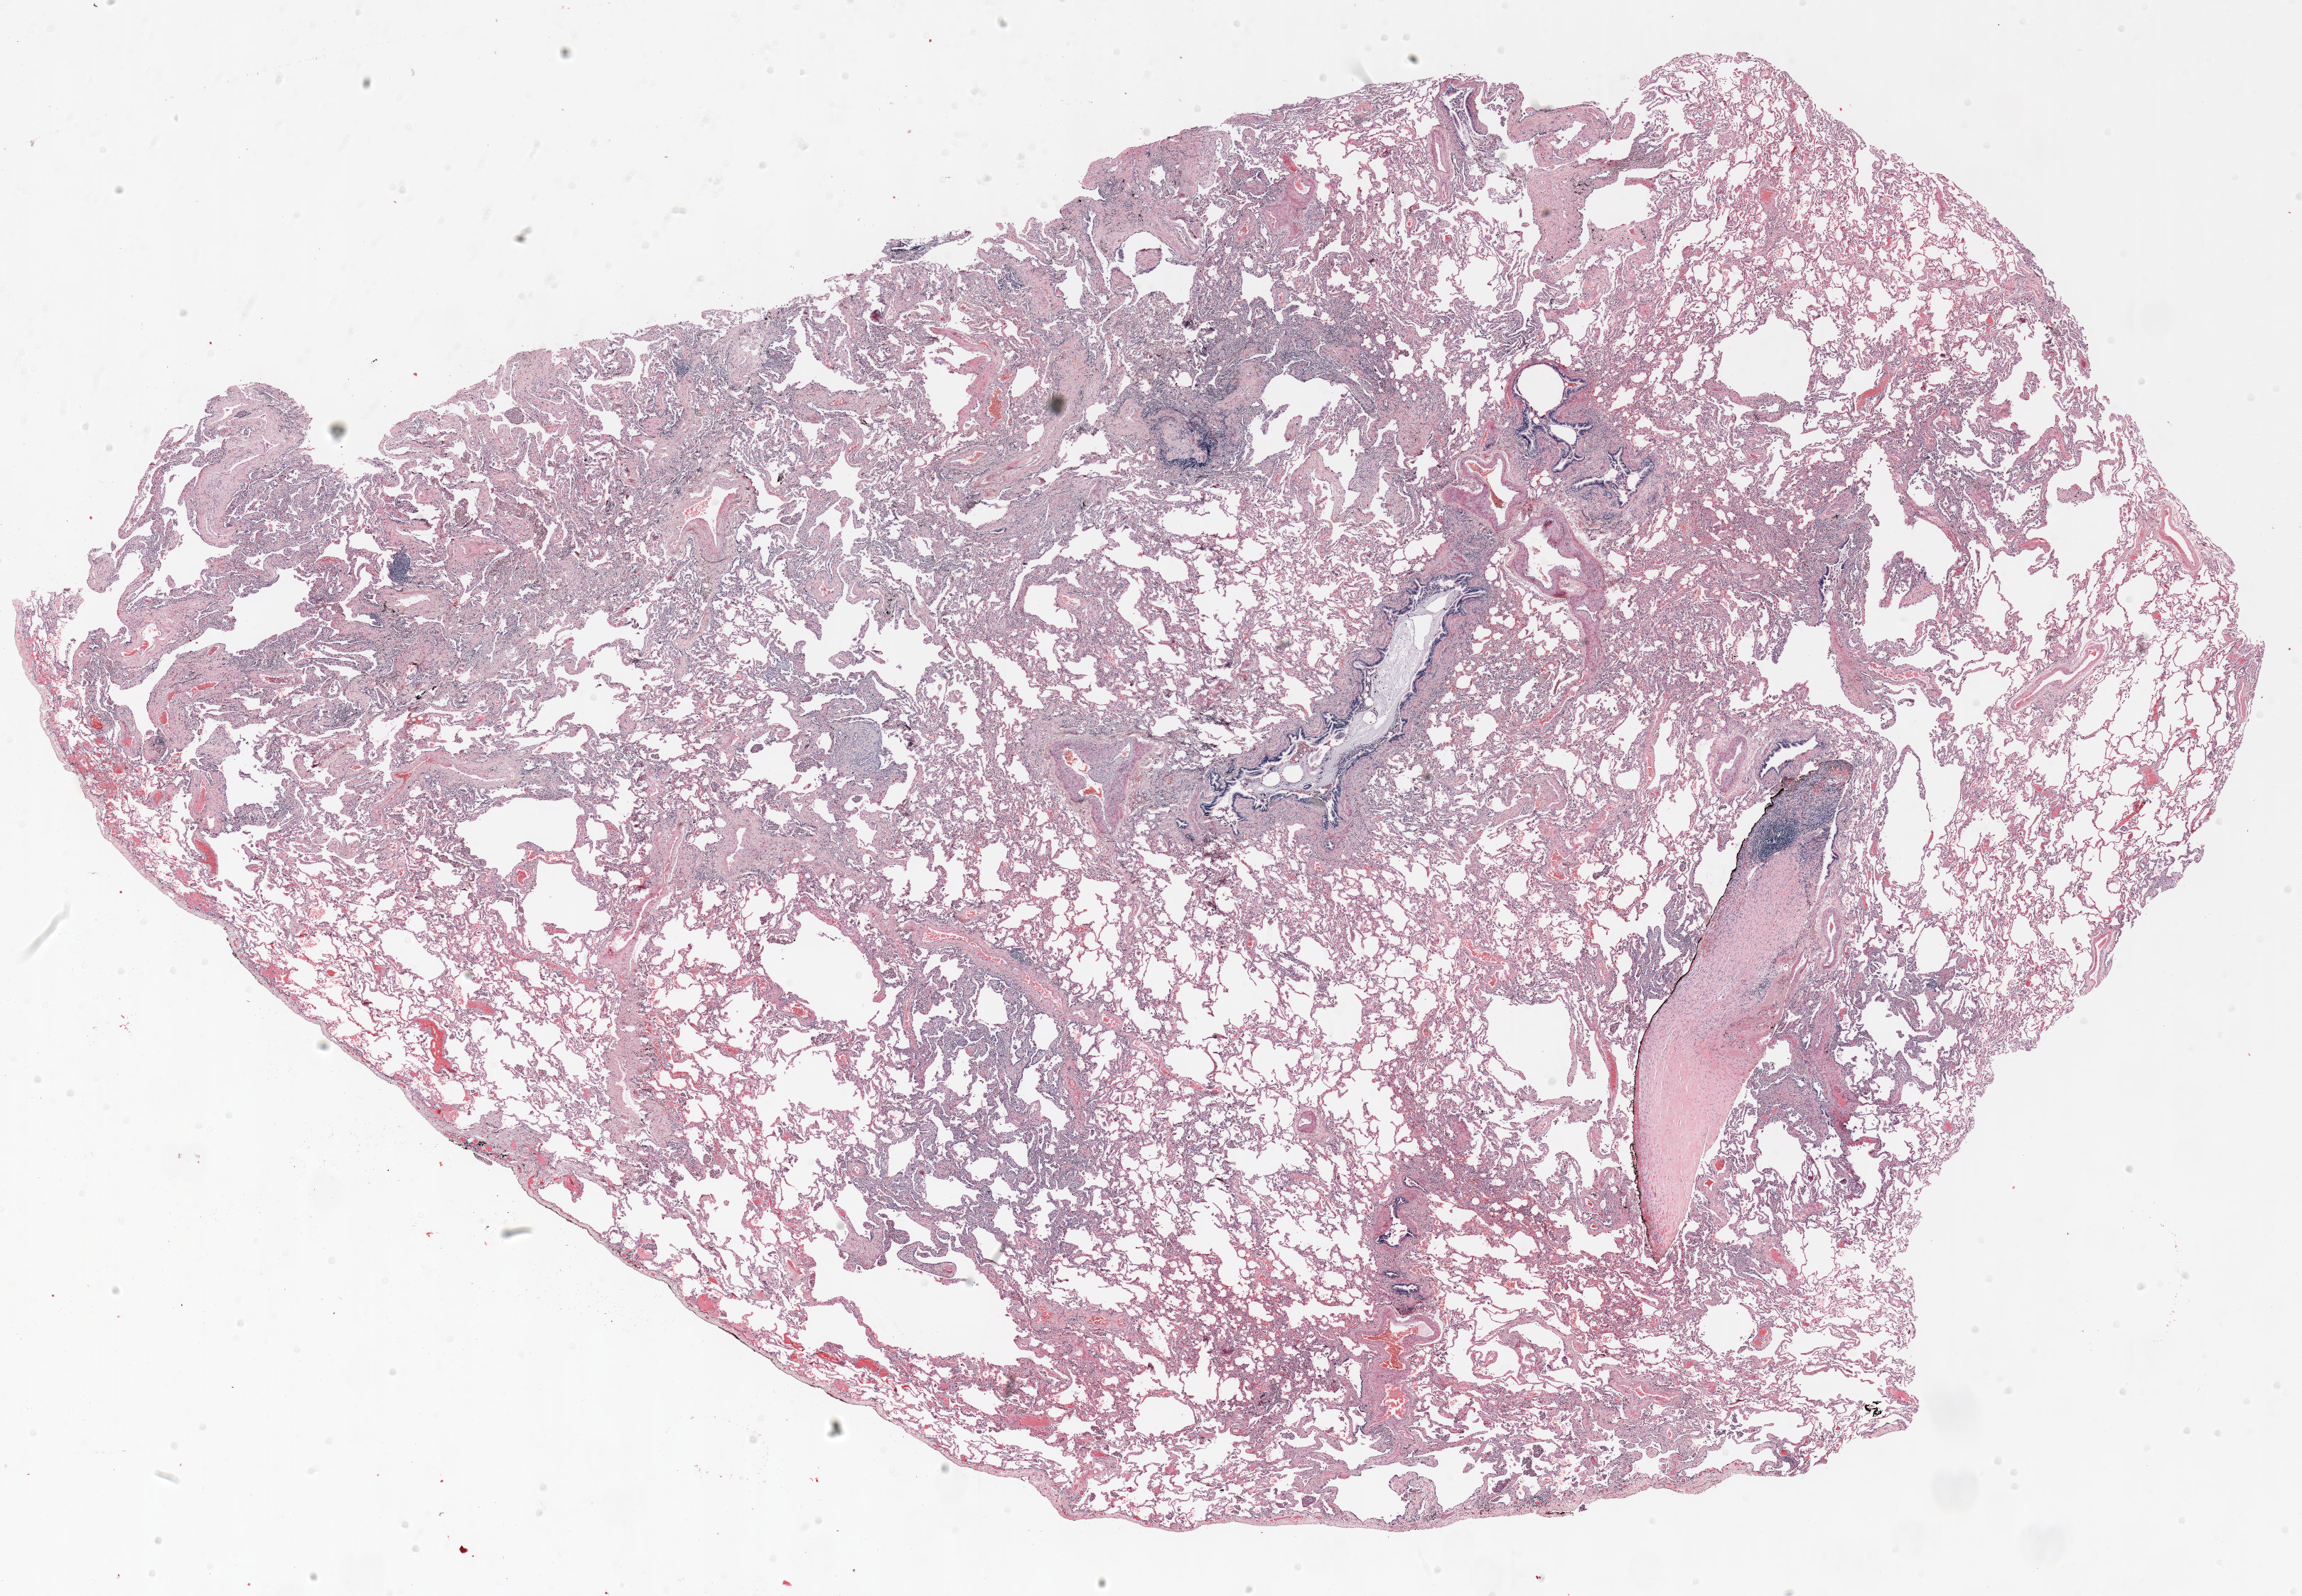
H&E whole-slide image, low-resolution overview of the scanned area, about 26.0 x 18.0 mm; formalin-fixed paraffin-embedded (FFPE) section; lung tissue. Female, age 56 at enrolment. Current smoker at enrolment. Grade: poorly differentiated (G3).
Primary tumour location (clinical record): right upper lobe. Participant's lung-cancer diagnosis: Large cell carcinoma, NOS. Tumour size (pathology): 15 mm. Stage (AJCC 6th edition): IB.